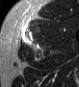
MRI of an extremity soft-tissue mass, one axial slice. Position 39 of 45 along the scan axis. STIR. MR volume resampled by the dataset authors to the PET/CT grid (not the native acquisition matrix). 3.27 mm slice thickness. 79 × 87 image matrix, field of view 77 × 85 mm. Male patient. From the clinical record (not read from this slice): histological type: pleiomorphic leiomyosarcoma; grade: high; site of the primary tumour: left thigh.
Annotated regions visible in this slice (expert contour drawn on MRI and transferred to this co-registered scan by the dataset authors):
- gross tumour volume including surrounding oedema: box from (x=24, y=32) to (x=37, y=47) px